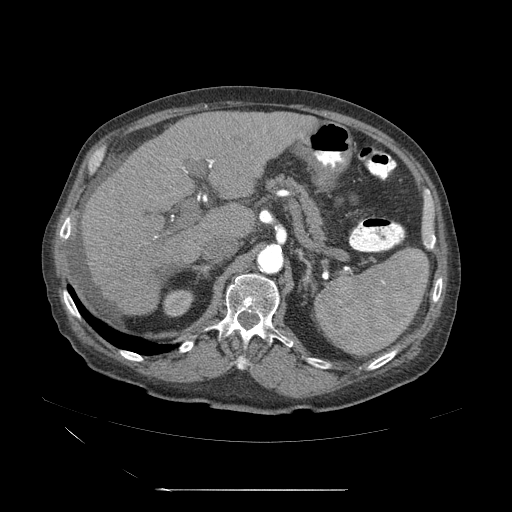
Contrast-enhanced abdominal CT (liver protocol), one axial slice; slice 28 of 71 in the series (ordered by position); reconstruction kernel STANDARD; soft-tissue window (W 400 / L 40 HU); 2.5 mm slice thickness; 512 × 512 image matrix. Case-level facts recorded for this patient, not image findings: diagnosis: hepatocellular carcinoma (patient treated with transarterial chemoembolisation; whether this scan precedes or follows treatment is not stated here); TNM stage (as recorded): Stage-II; Child-Pugh class: A.
Outlined on this slice (semi-automatic segmentation, software-assisted and operator-edited):
- abdominal aorta: box from (x=258, y=246) to (x=284, y=275) px
- liver parenchyma outside the tumour (the mass and vessels are separate outlines, so this box may not span the whole liver): (x=77, y=113)–(x=301, y=319)
- liver vessels: (x=136, y=161)–(x=239, y=264)